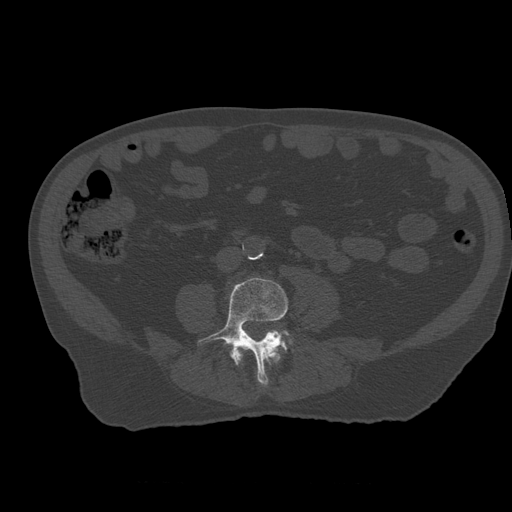
CT including the spine, one axial slice; position 166 of 399 along the scan axis; reconstruction kernel STANDARD; 120 kVp; bone window (W 1800 / L 400 HU); 1.25 mm slice thickness; 512 × 512 image matrix, field of view 407 × 407 mm. Patient age 73 years. Case-level facts recorded for this patient, not image findings: primary cancer: prostate; vertebrae with lytic lesions (as recorded): L2.
Outlined on this slice (semi-automatically segmented with operator editing):
- L3 vertebra: box from (x=236, y=345) to (x=281, y=364) px
- L4 vertebra: (x=198, y=278)–(x=291, y=385)